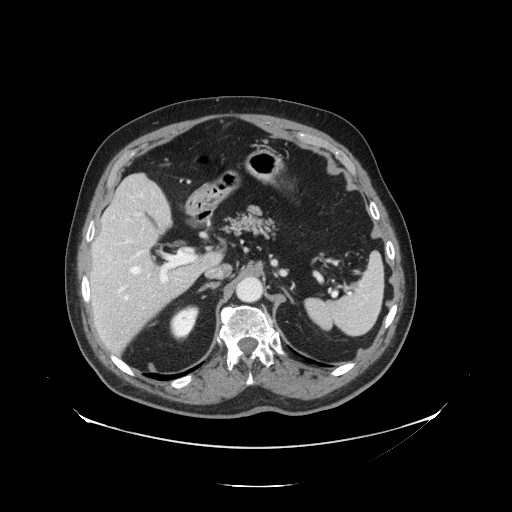
Contrast-enhanced abdominal CT, one axial slice. Position 86 of 138 along the scan axis. Reconstruction kernel STANDARD. Intravenous contrast given. Soft-tissue window (W 400 / L 40 HU). 2.5 mm slice thickness. 512 × 512 image matrix, field of view 497 × 497 mm. Male patient, age 77 years. From the clinical record (not read from this slice): diagnosis: colorectal cancer liver metastases, imaged before liver resection.
Annotated regions visible in this slice (manually delineated by an expert):
- hepatic veins: bounding box [x1, y1, x2, y2] px = [130, 266, 141, 275]
- liver: [90, 175, 219, 355]
- planned liver remnant (the part of the liver to remain after resection): [92, 175, 172, 287]
- portal vein (with intrahepatic branches): [116, 250, 195, 301]